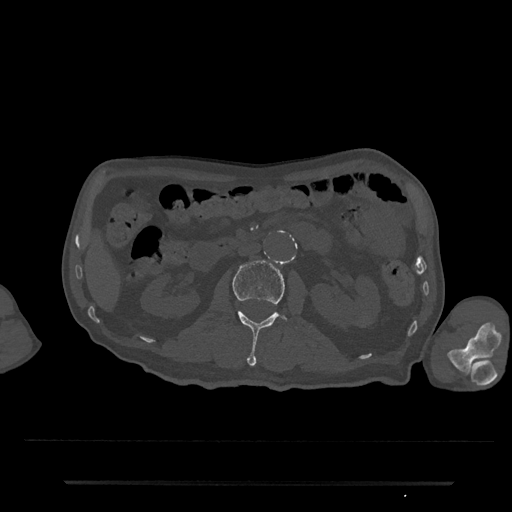
CT including the spine, one axial slice. Position 55 of 797 along the scan axis. Reconstruction kernel Br40s/3. Bone window (W 1800 / L 400 HU). 0.5 mm slice thickness. 512 × 512 image matrix, field of view 427 × 427 mm. Patient: male, 74 years. From the clinical record (not read from this slice): primary cancer: prostate.
Structures marked on this image (semi-automatically segmented with operator editing):
- L2 vertebra: box from (x=233, y=260) to (x=297, y=366) px